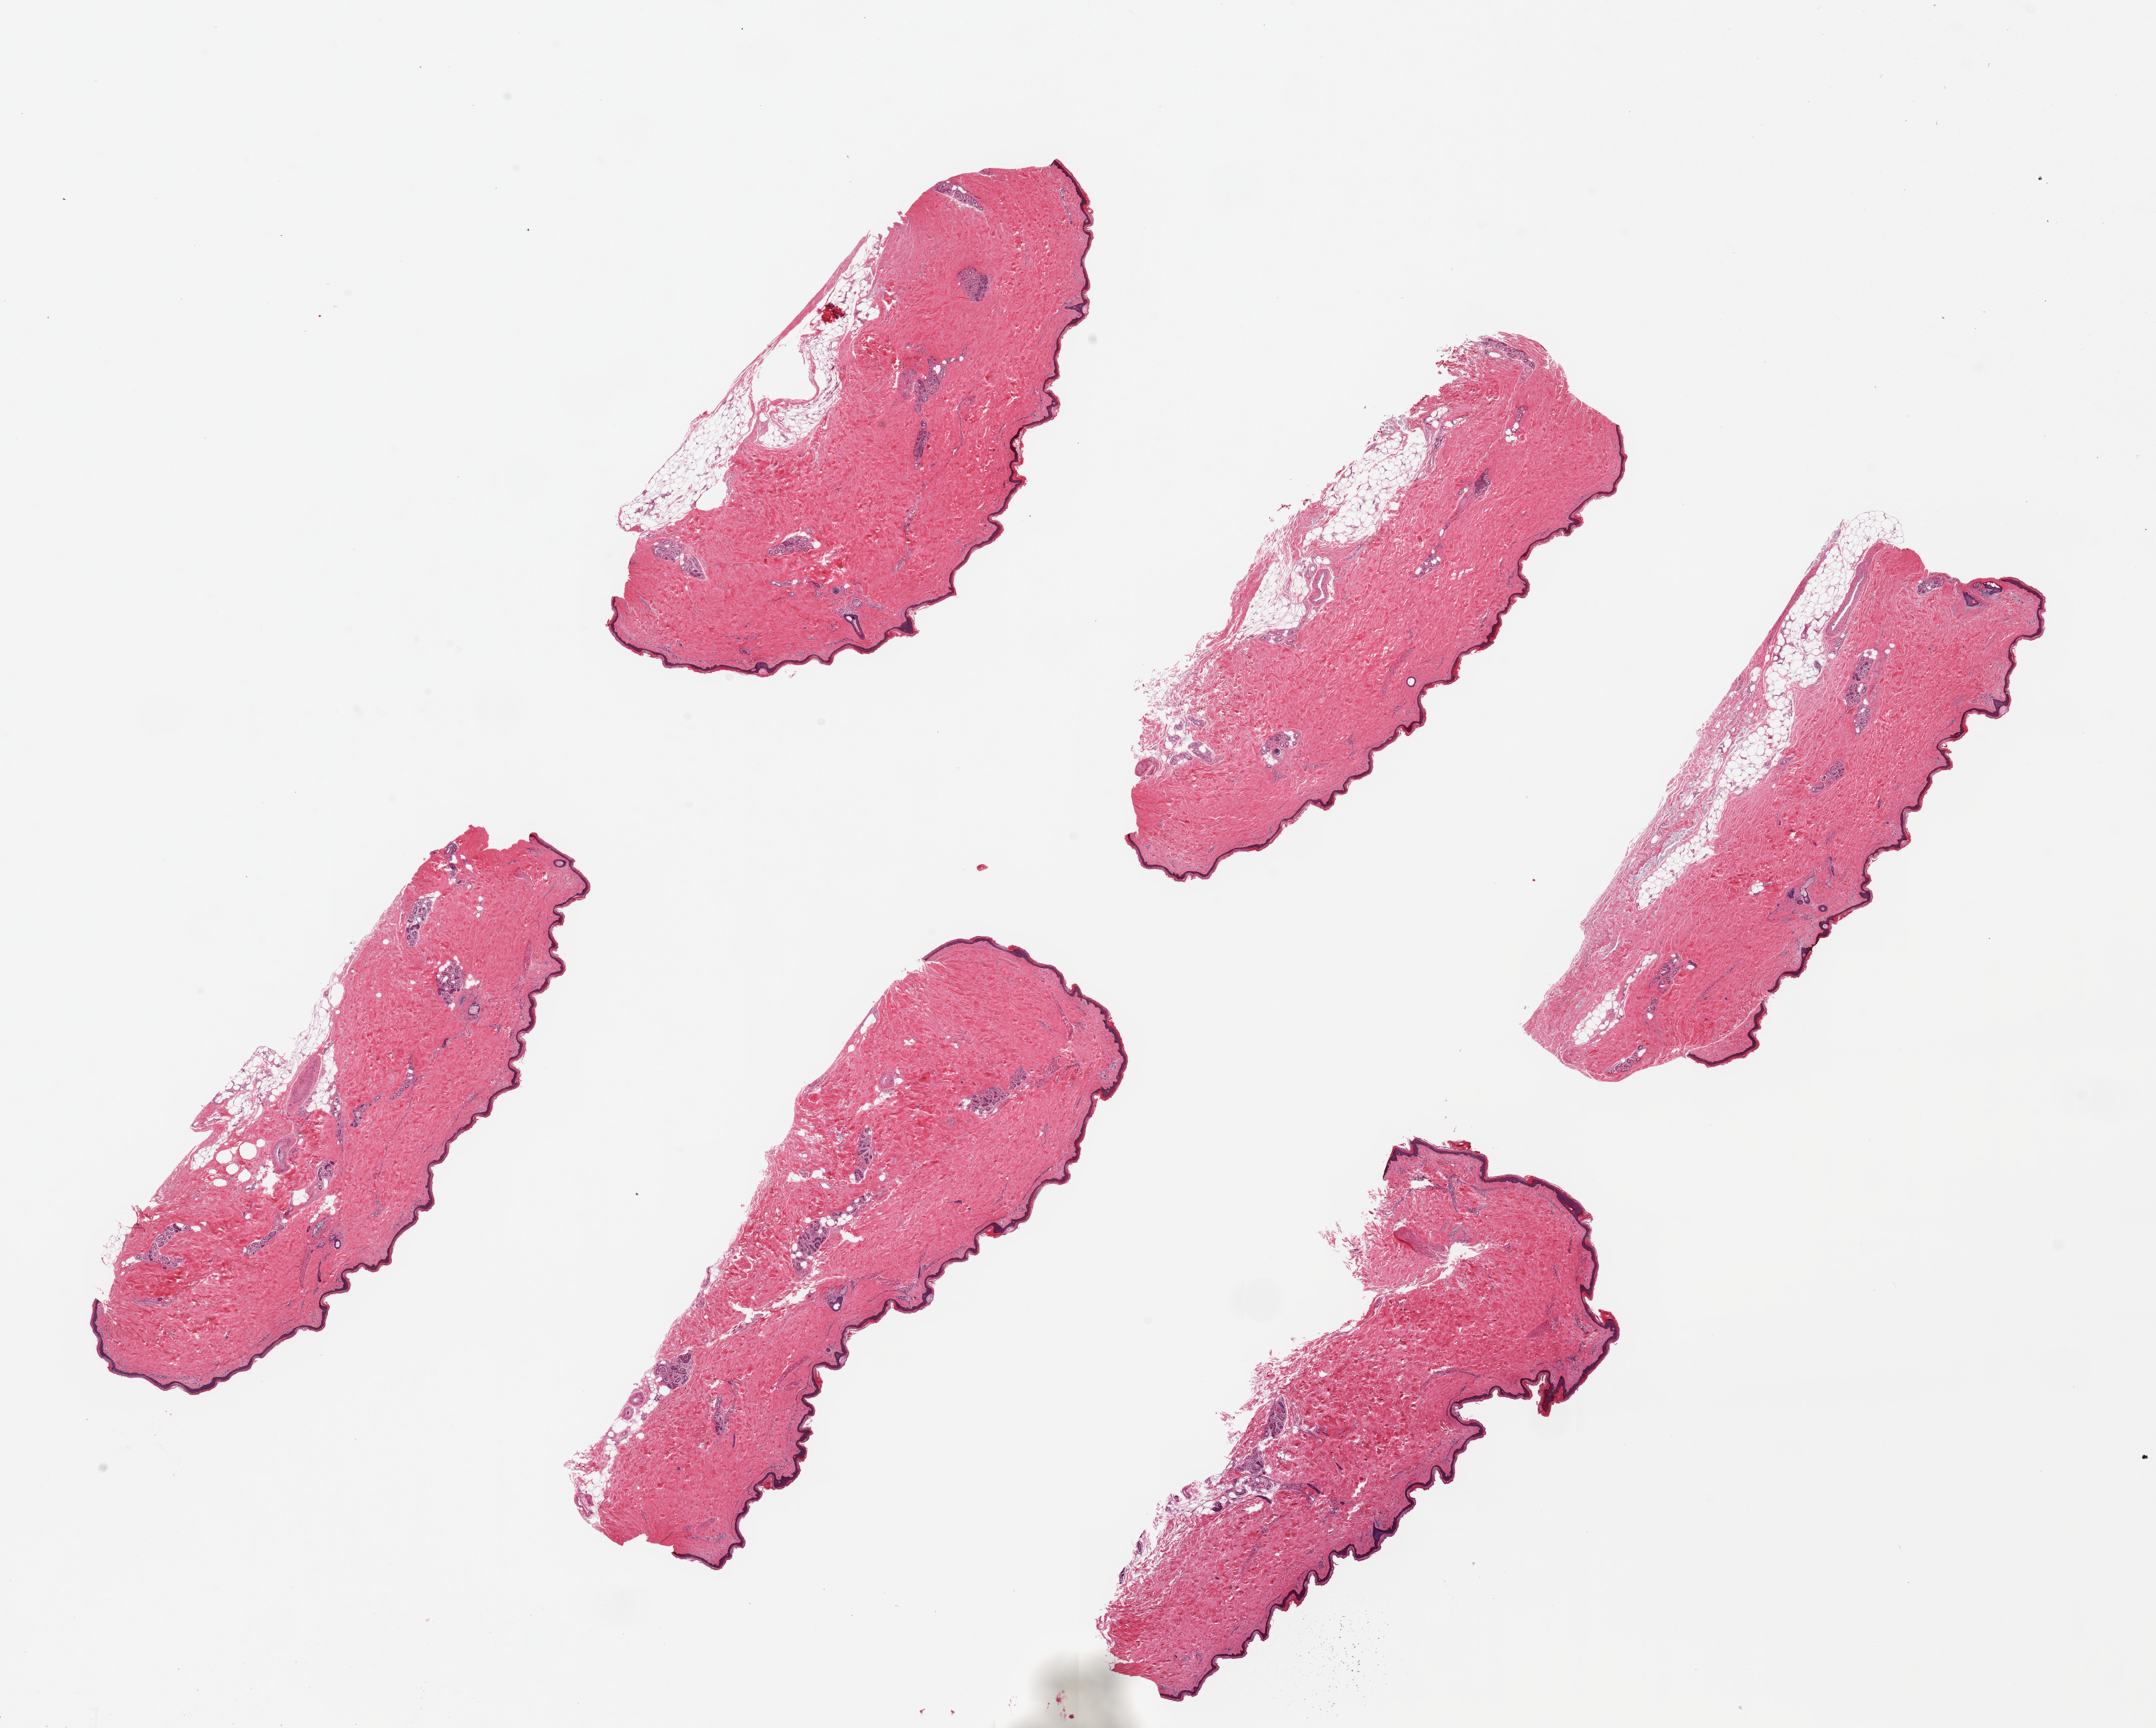
Hematoxylin and eosin (H&E) whole-slide image, whole scanned area (about 25.6 x 20.5 mm) shown as a low-resolution overview; PAXgene-fixed paraffin-embedded (PFPE) section; sampled site (target tissue): skin of lower leg; tissue donor sample. Donor: male.
Review note (as recorded): 6 pieces up to 8x3.5 mm; subcutaneous adipose up to 0.6mm.